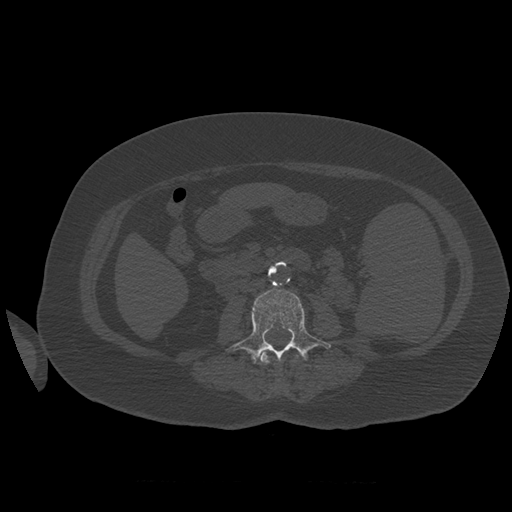
CT including the spine, one axial slice. Position 233 of 399 along the scan axis. Reconstruction kernel STANDARD. 120 kVp. Bone window (W 1800 / L 400 HU). 512 × 512 image matrix. Patient age 81 years. From the clinical record (not read from this slice): primary cancer: renal; vertebrae with lytic lesions (as recorded): L1.
Annotated regions visible in this slice (semi-automatic segmentation, software-assisted and operator-edited):
- L2 vertebra: bounding box <257,351,299,365> (left, top, right, bottom; pixels)
- L3 vertebra: <226,288,331,363>